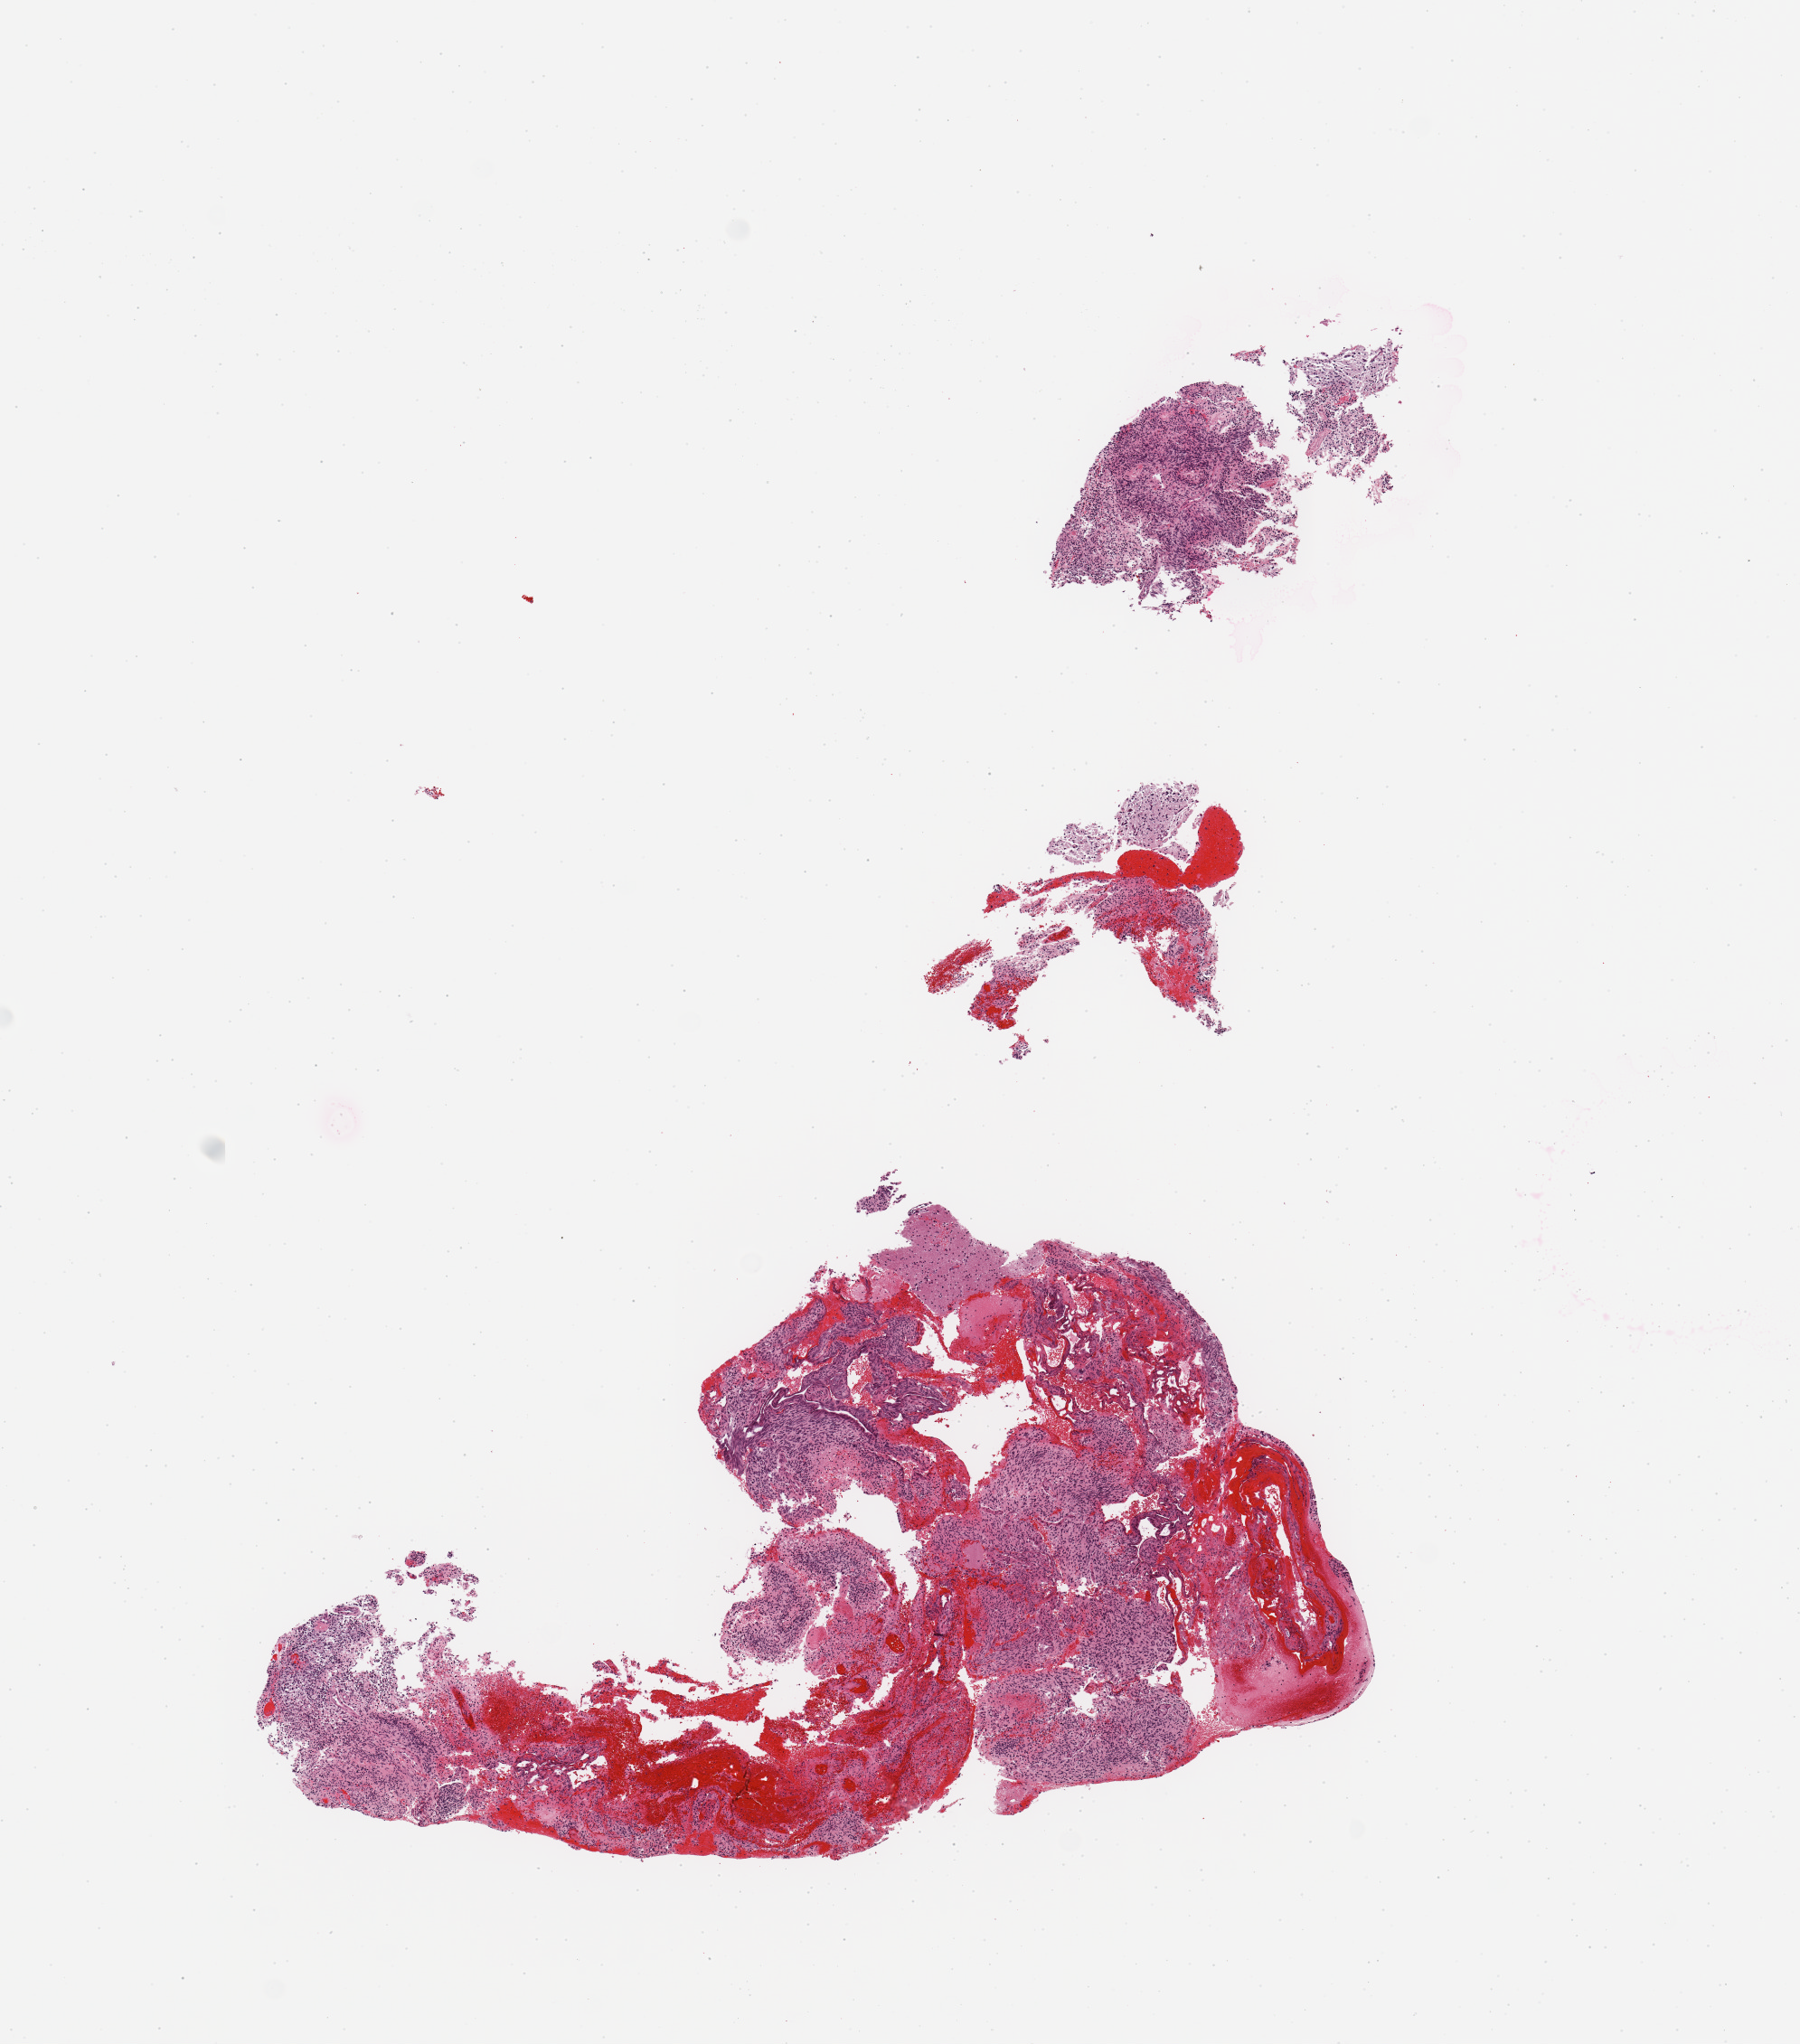
Digitized H&E tissue section (whole slide), shown as a low-resolution overview of the whole scanned area (about 7.9 x 8.9 mm, acquisition: 20x scan). Tumour tissue sample, sampled site: temporal cortex. Patient: male, age 48 years. Composition of this section per pathologist review: tumour nuclei 80%, necrosis 30%.
• histologic diagnosis: Glioblastoma